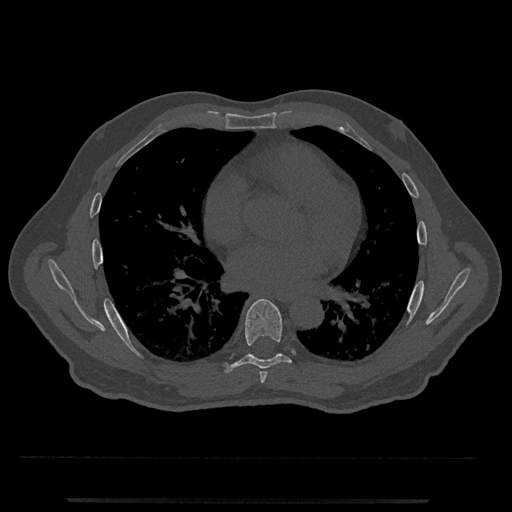
CT including the spine, one axial slice; position 684 of 797 along the scan axis; bone window (W 1800 / L 400 HU); 0.5 mm slice thickness; 512 × 512 image matrix. Patient: male, 63 years. From the clinical record (not read from this slice): primary cancer: prostate.
Annotated regions visible in this slice (semi-automatically segmented with operator editing):
- T6 vertebra: box from (x=259, y=371) to (x=267, y=383) px
- T7 vertebra: (x=220, y=299)–(x=292, y=374)